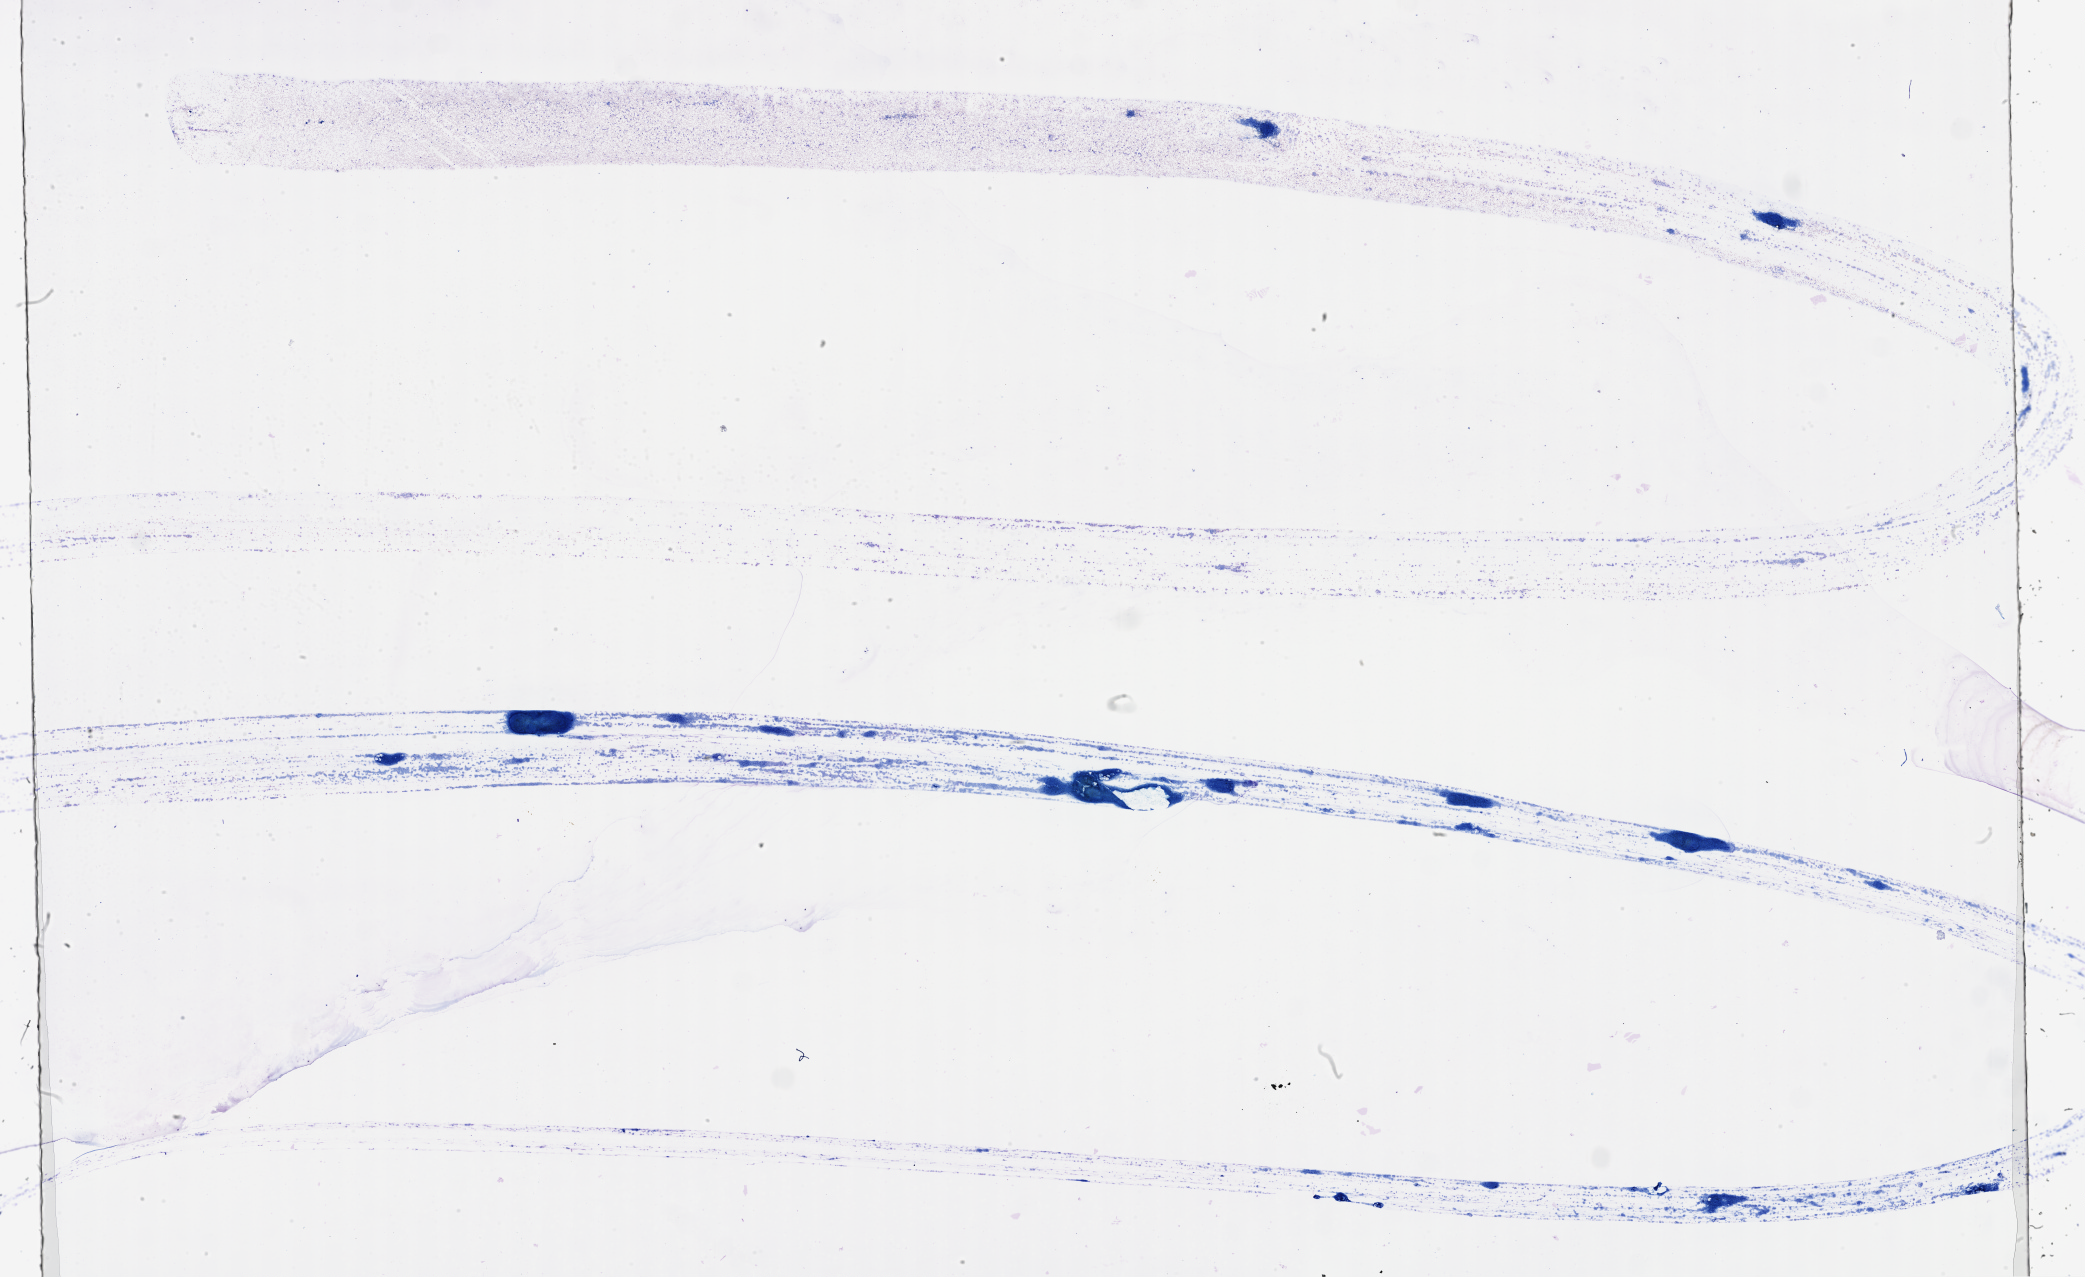
Whole-slide histology image, H&E — whole scanned area (about 33.7 x 20.6 mm, acquisition: 40x scan) shown as a low-resolution overview. Bone marrow (leukaemic) sample. Patient: female, age 48 years. Blasts: 90%.
• diagnosis: Acute Myeloid Leukemia
• WHO classification: Acute myelomonocytic leukemia
• FAB classification: M4